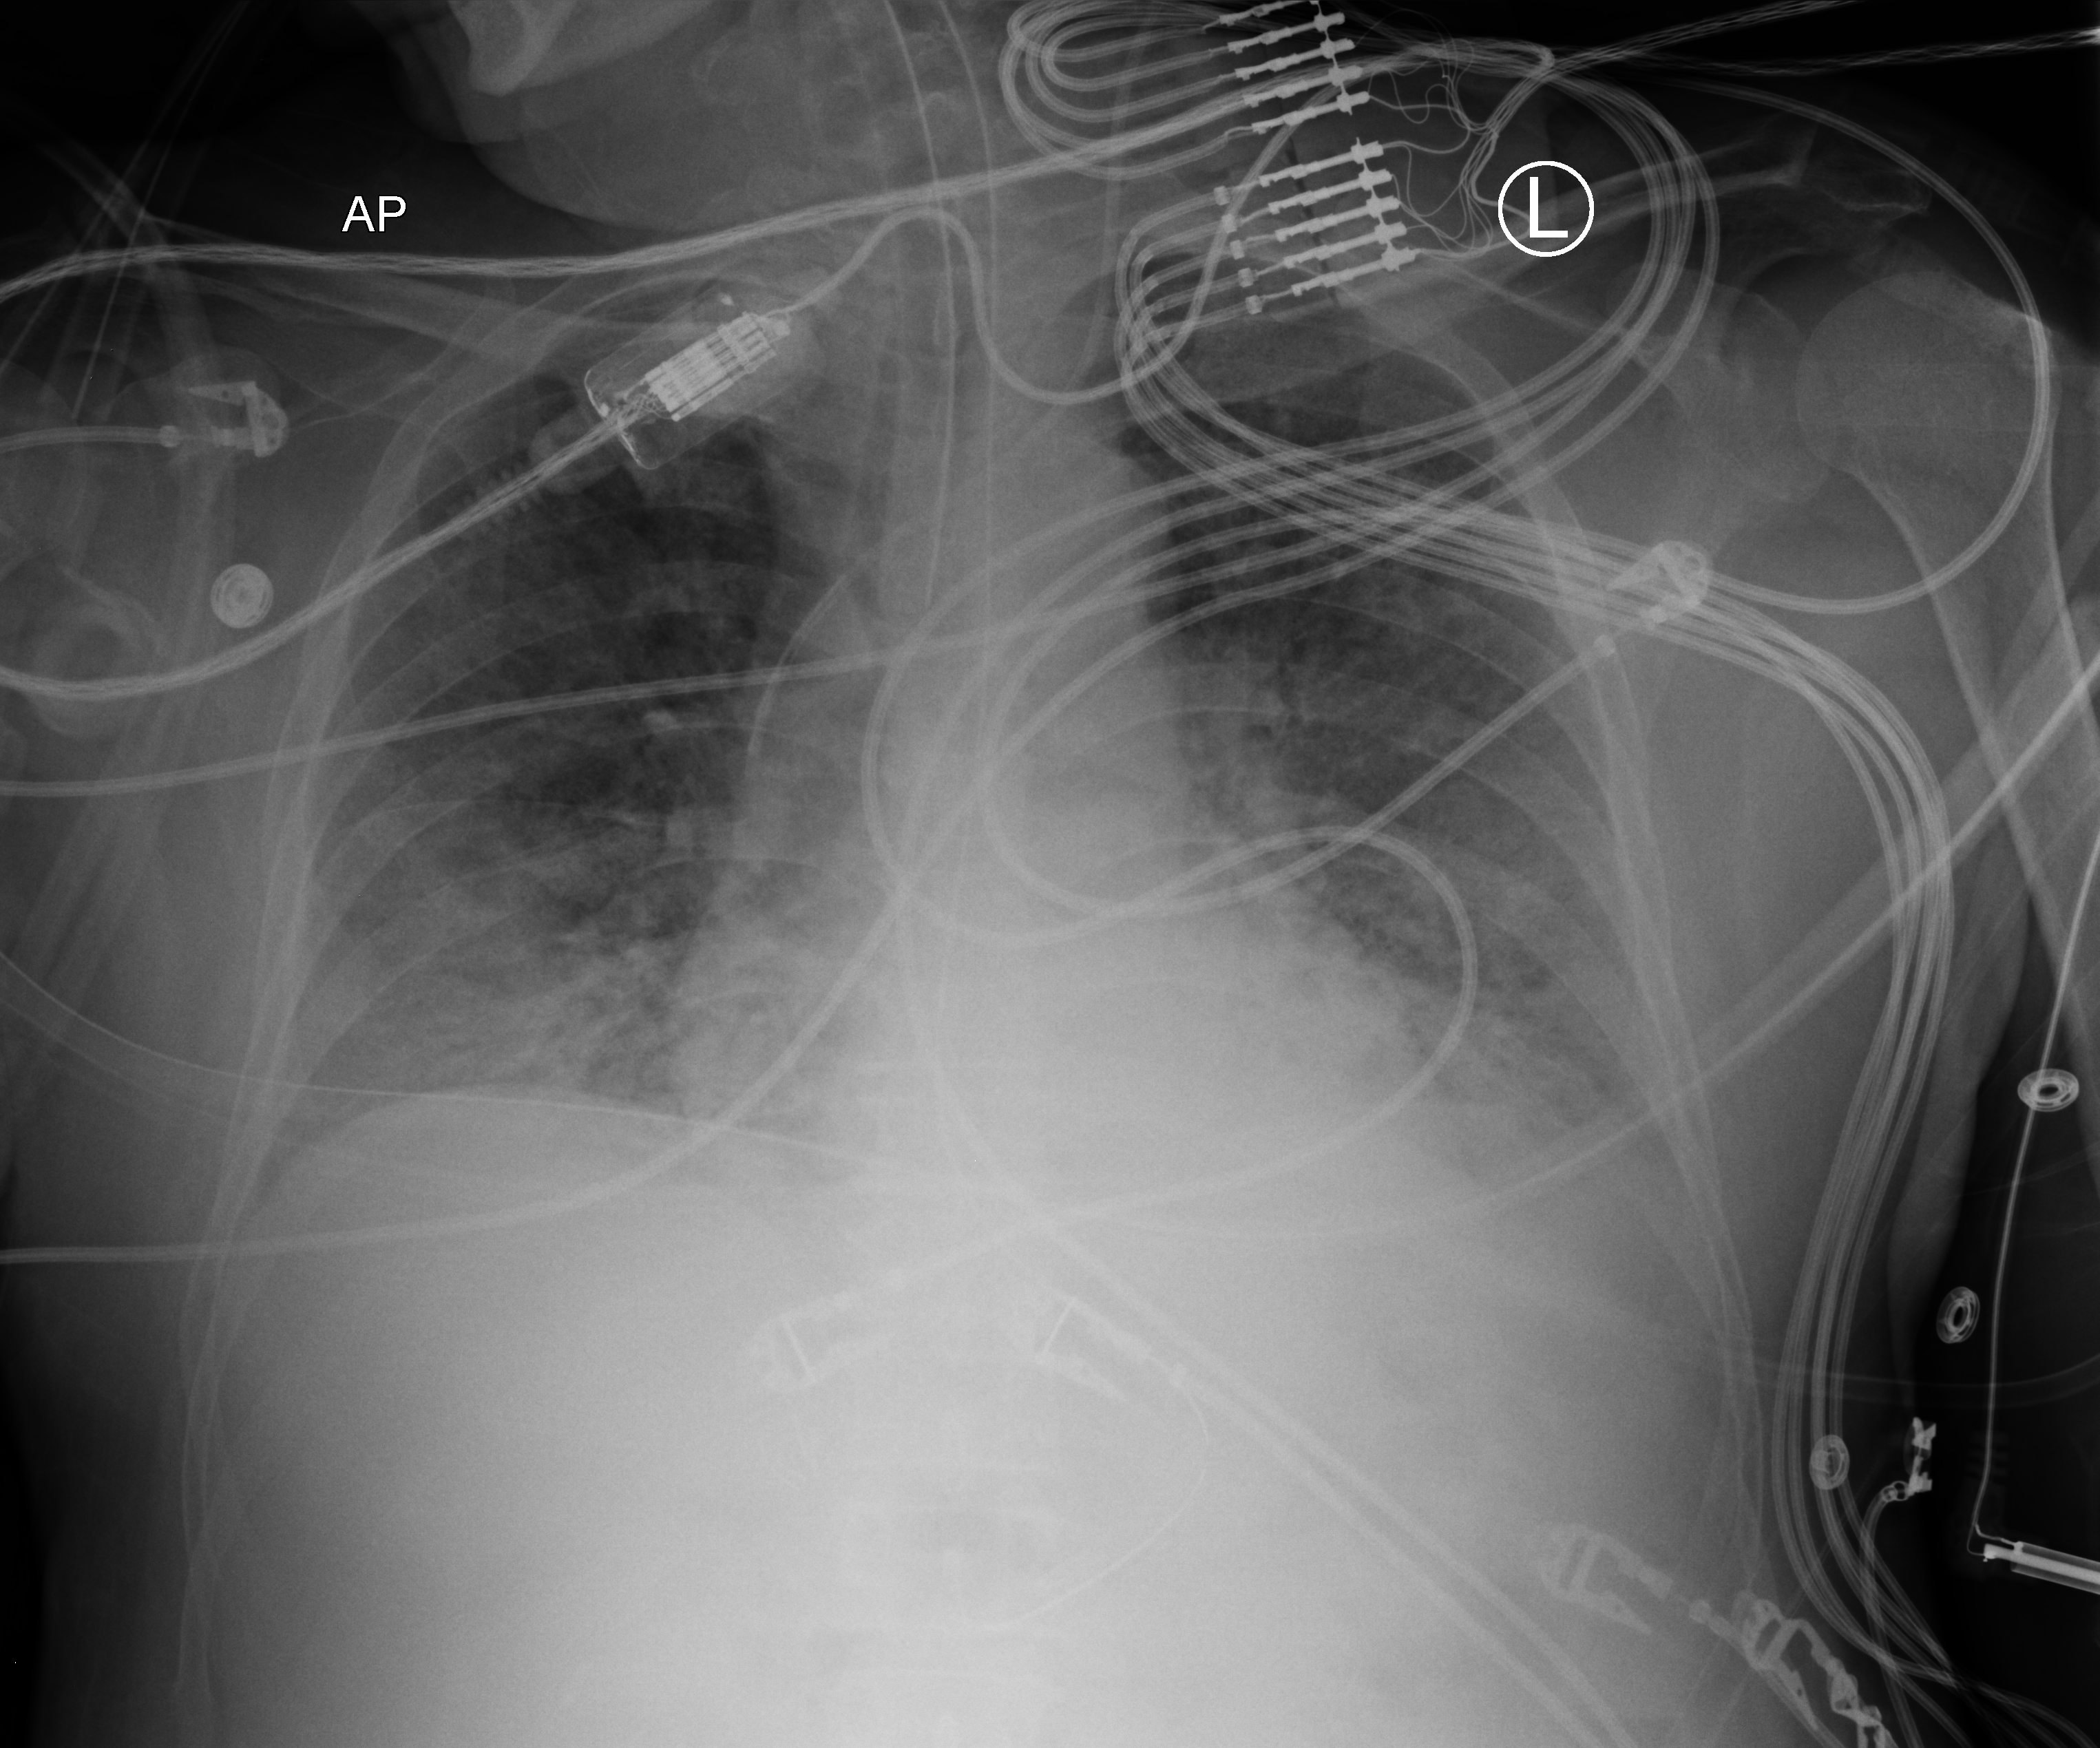
Chest X-ray (portable); anteroposterior (AP) projection. Patient hospitalised with COVID-19; male, aged 60–74 years.
Admission-level facts for this patient (not findings on this image; timing relative to this image not recorded):
- admitted to intensive care during this hospital stay: yes
- other chronic lung disease (admission record): no